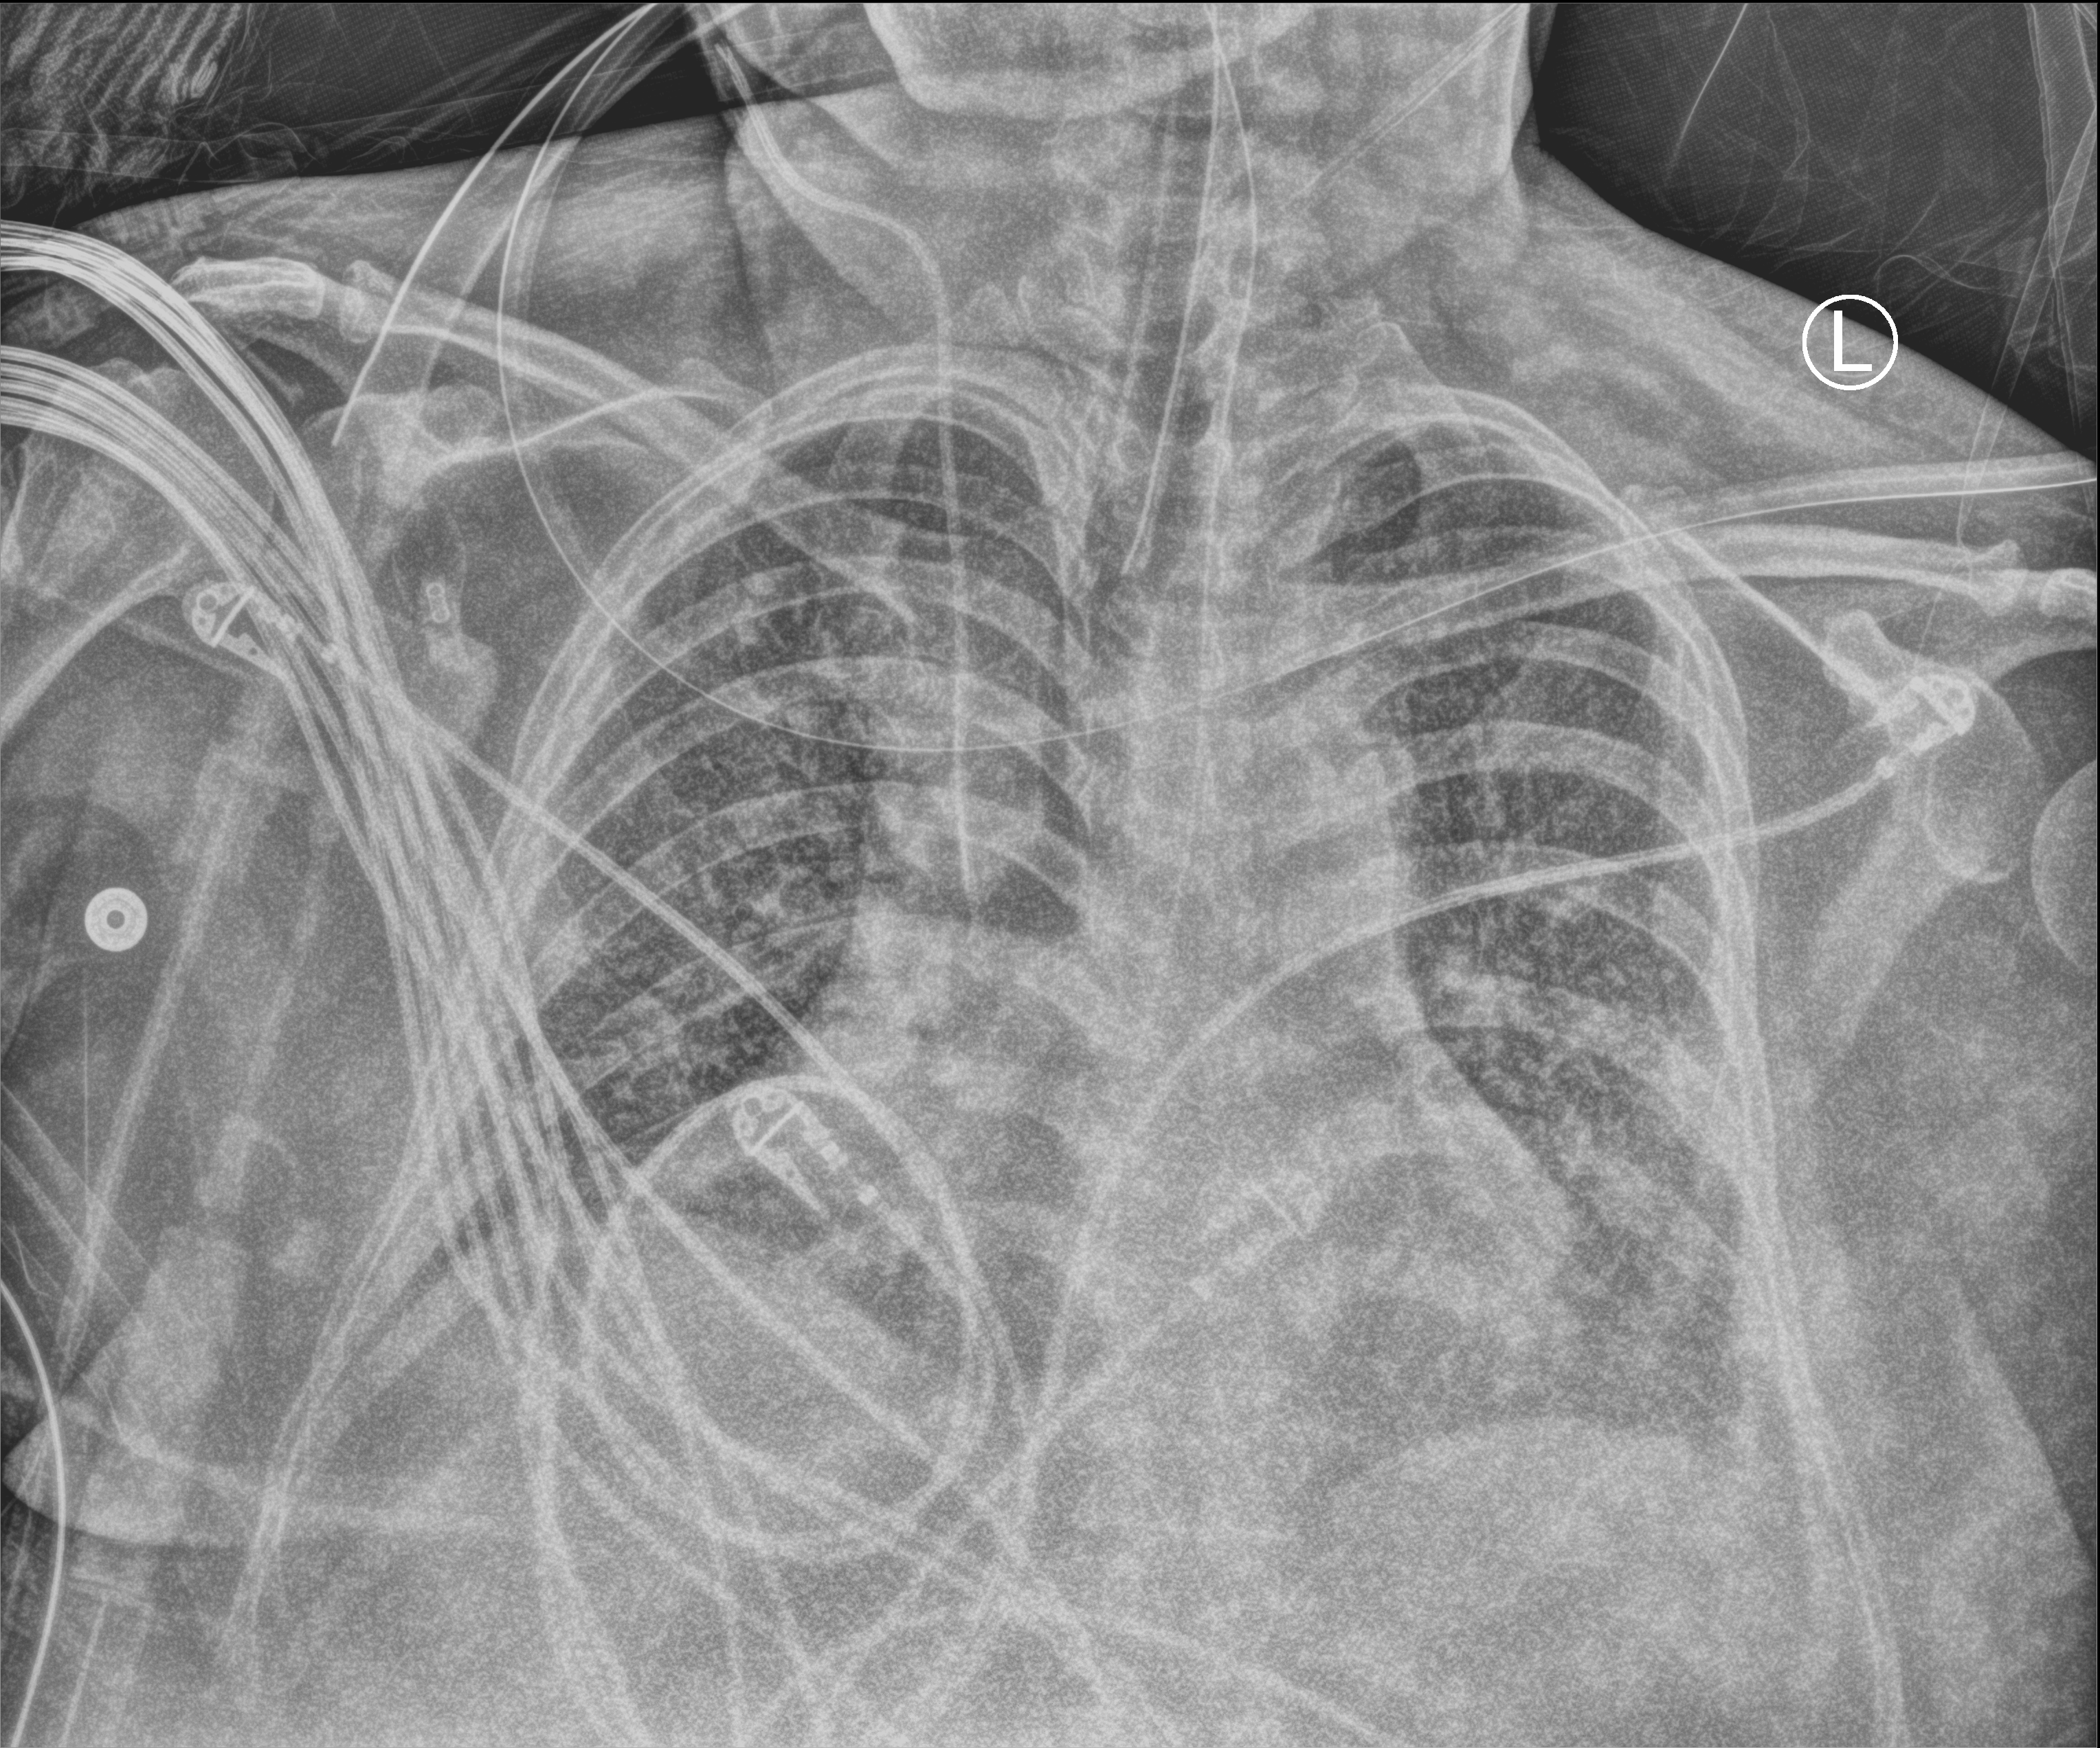
Chest X-ray (portable), anteroposterior (AP) projection. Patient hospitalised with COVID-19, aged 18–59 years.
From the hospital-stay record, not from the radiograph (when in the stay this image was taken is not recorded): chronic kidney disease (admission record): no.